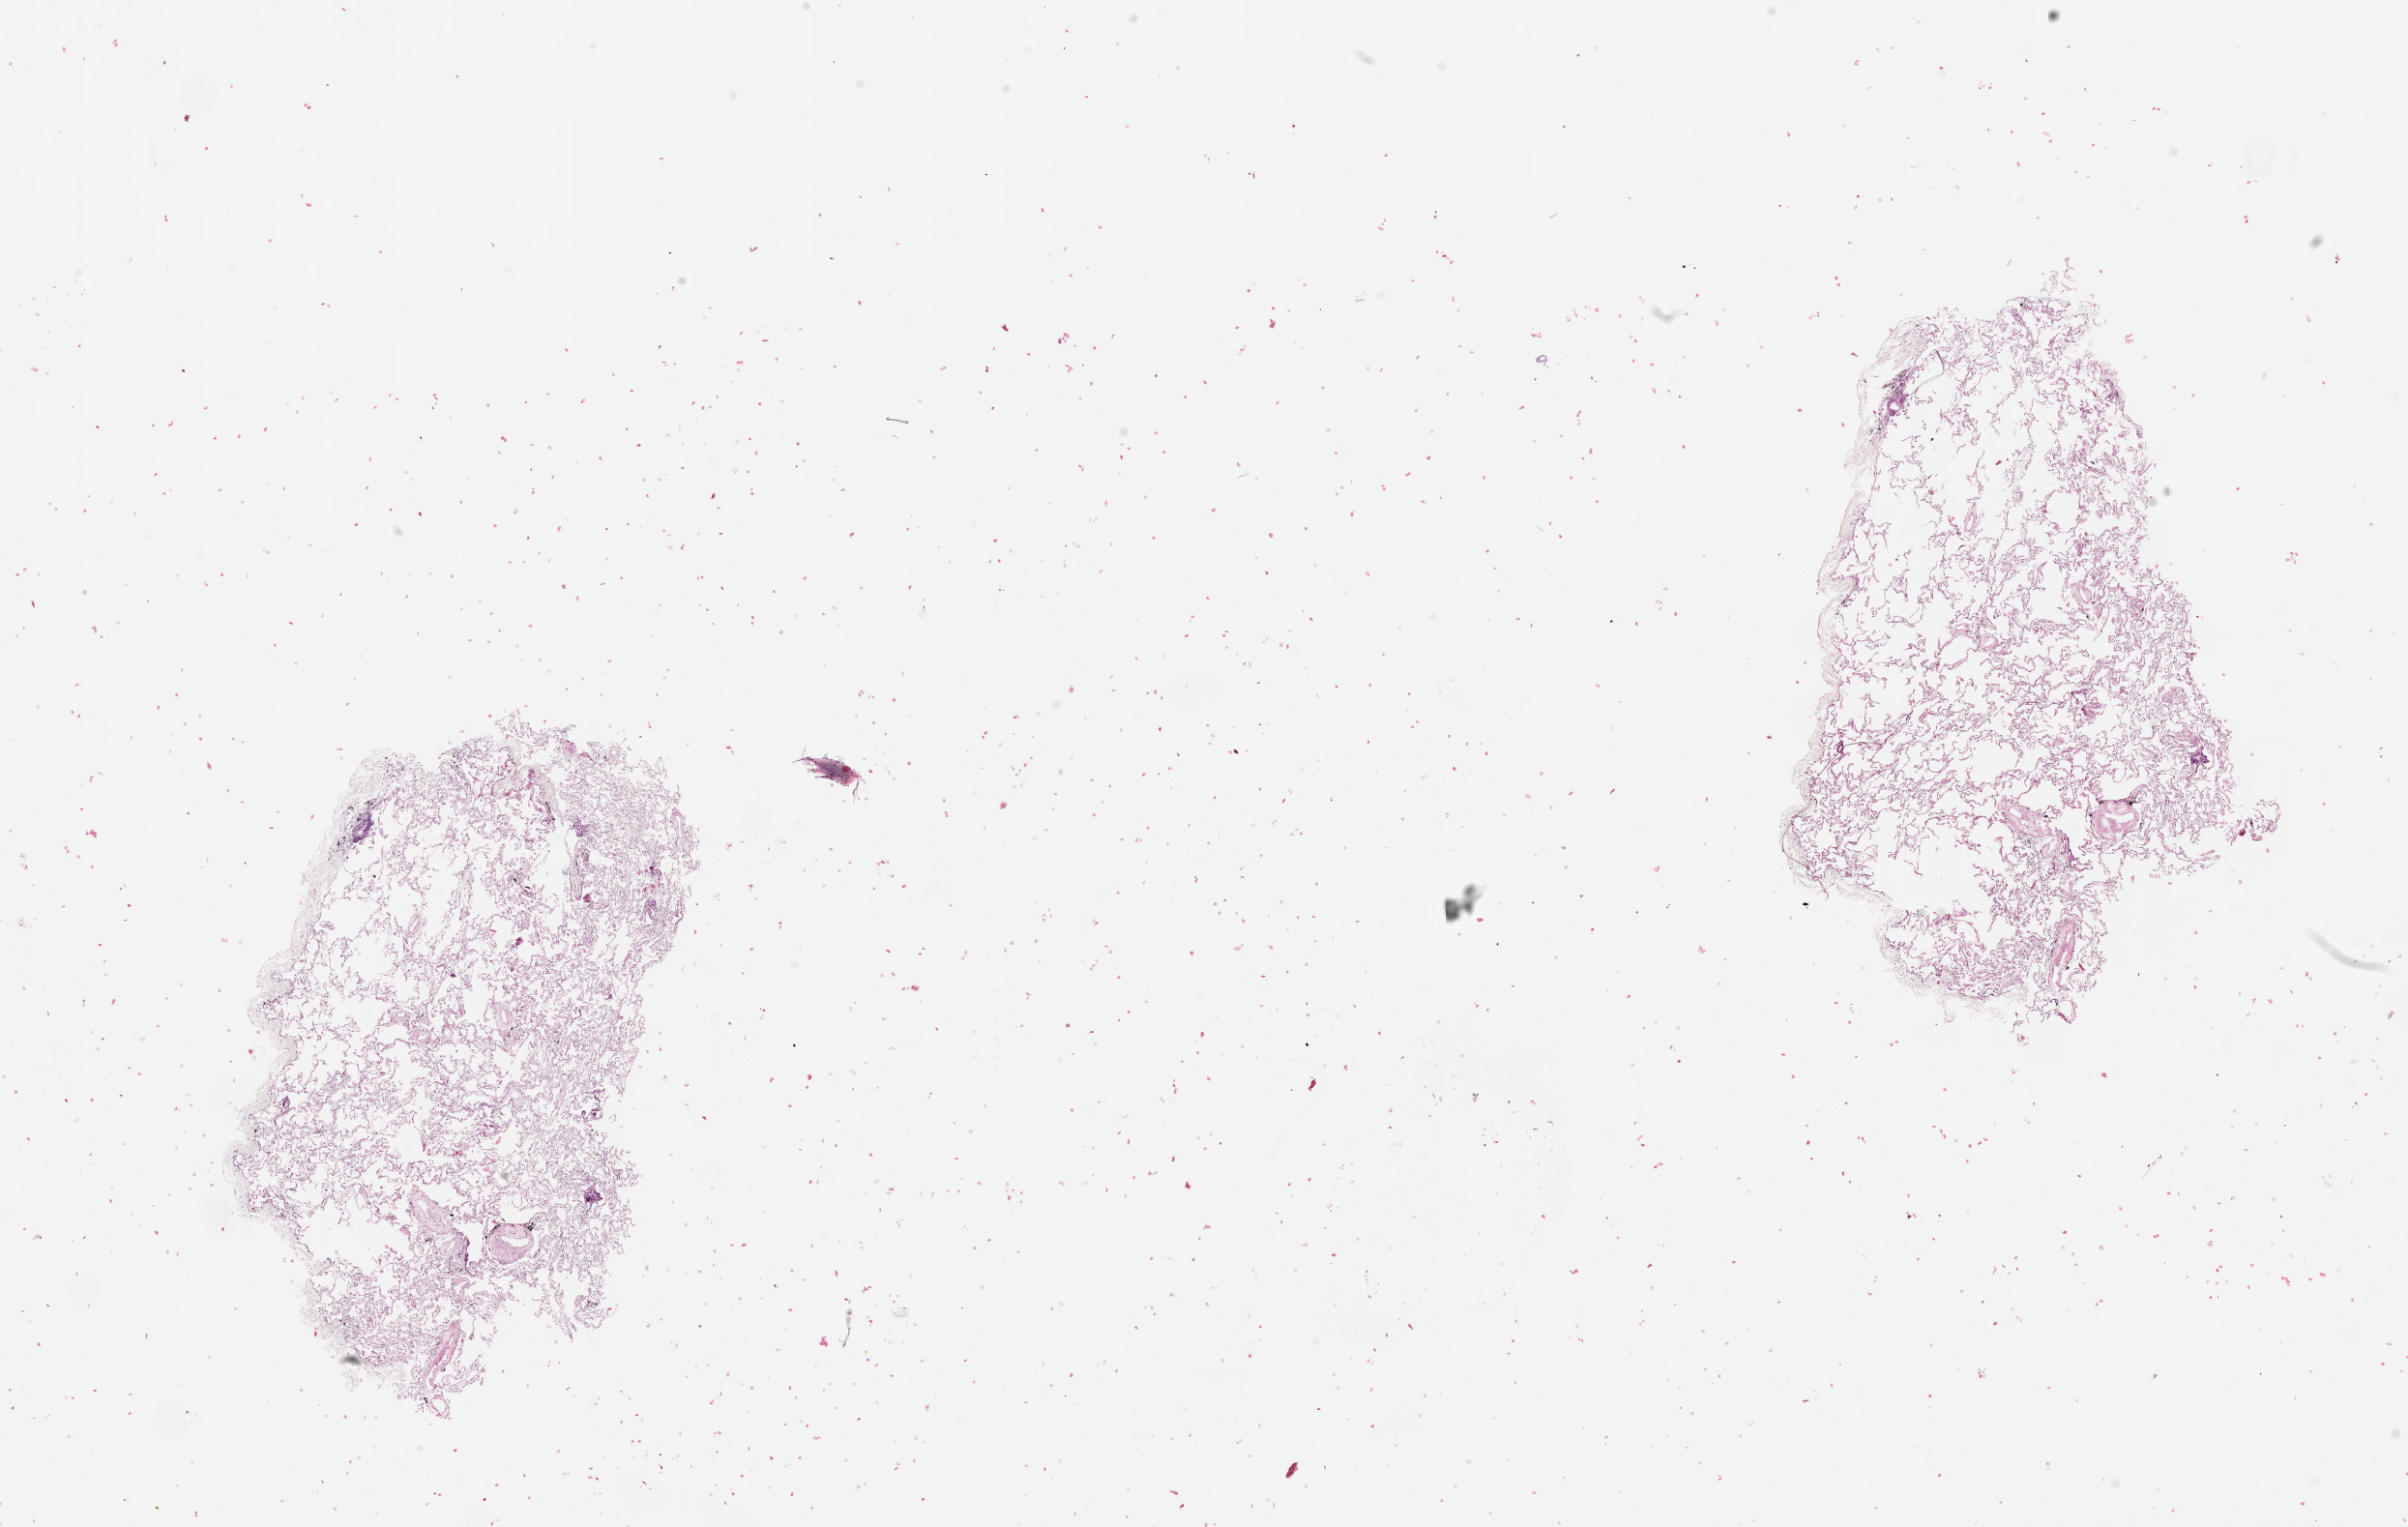
H&E whole-slide image — shown as a low-resolution overview of the whole scanned area (about 20.0 x 12.7 mm). Lung, tissue type not recorded.
• patient diagnosis (cohort enrolment): lung adenocarcinoma (lung)